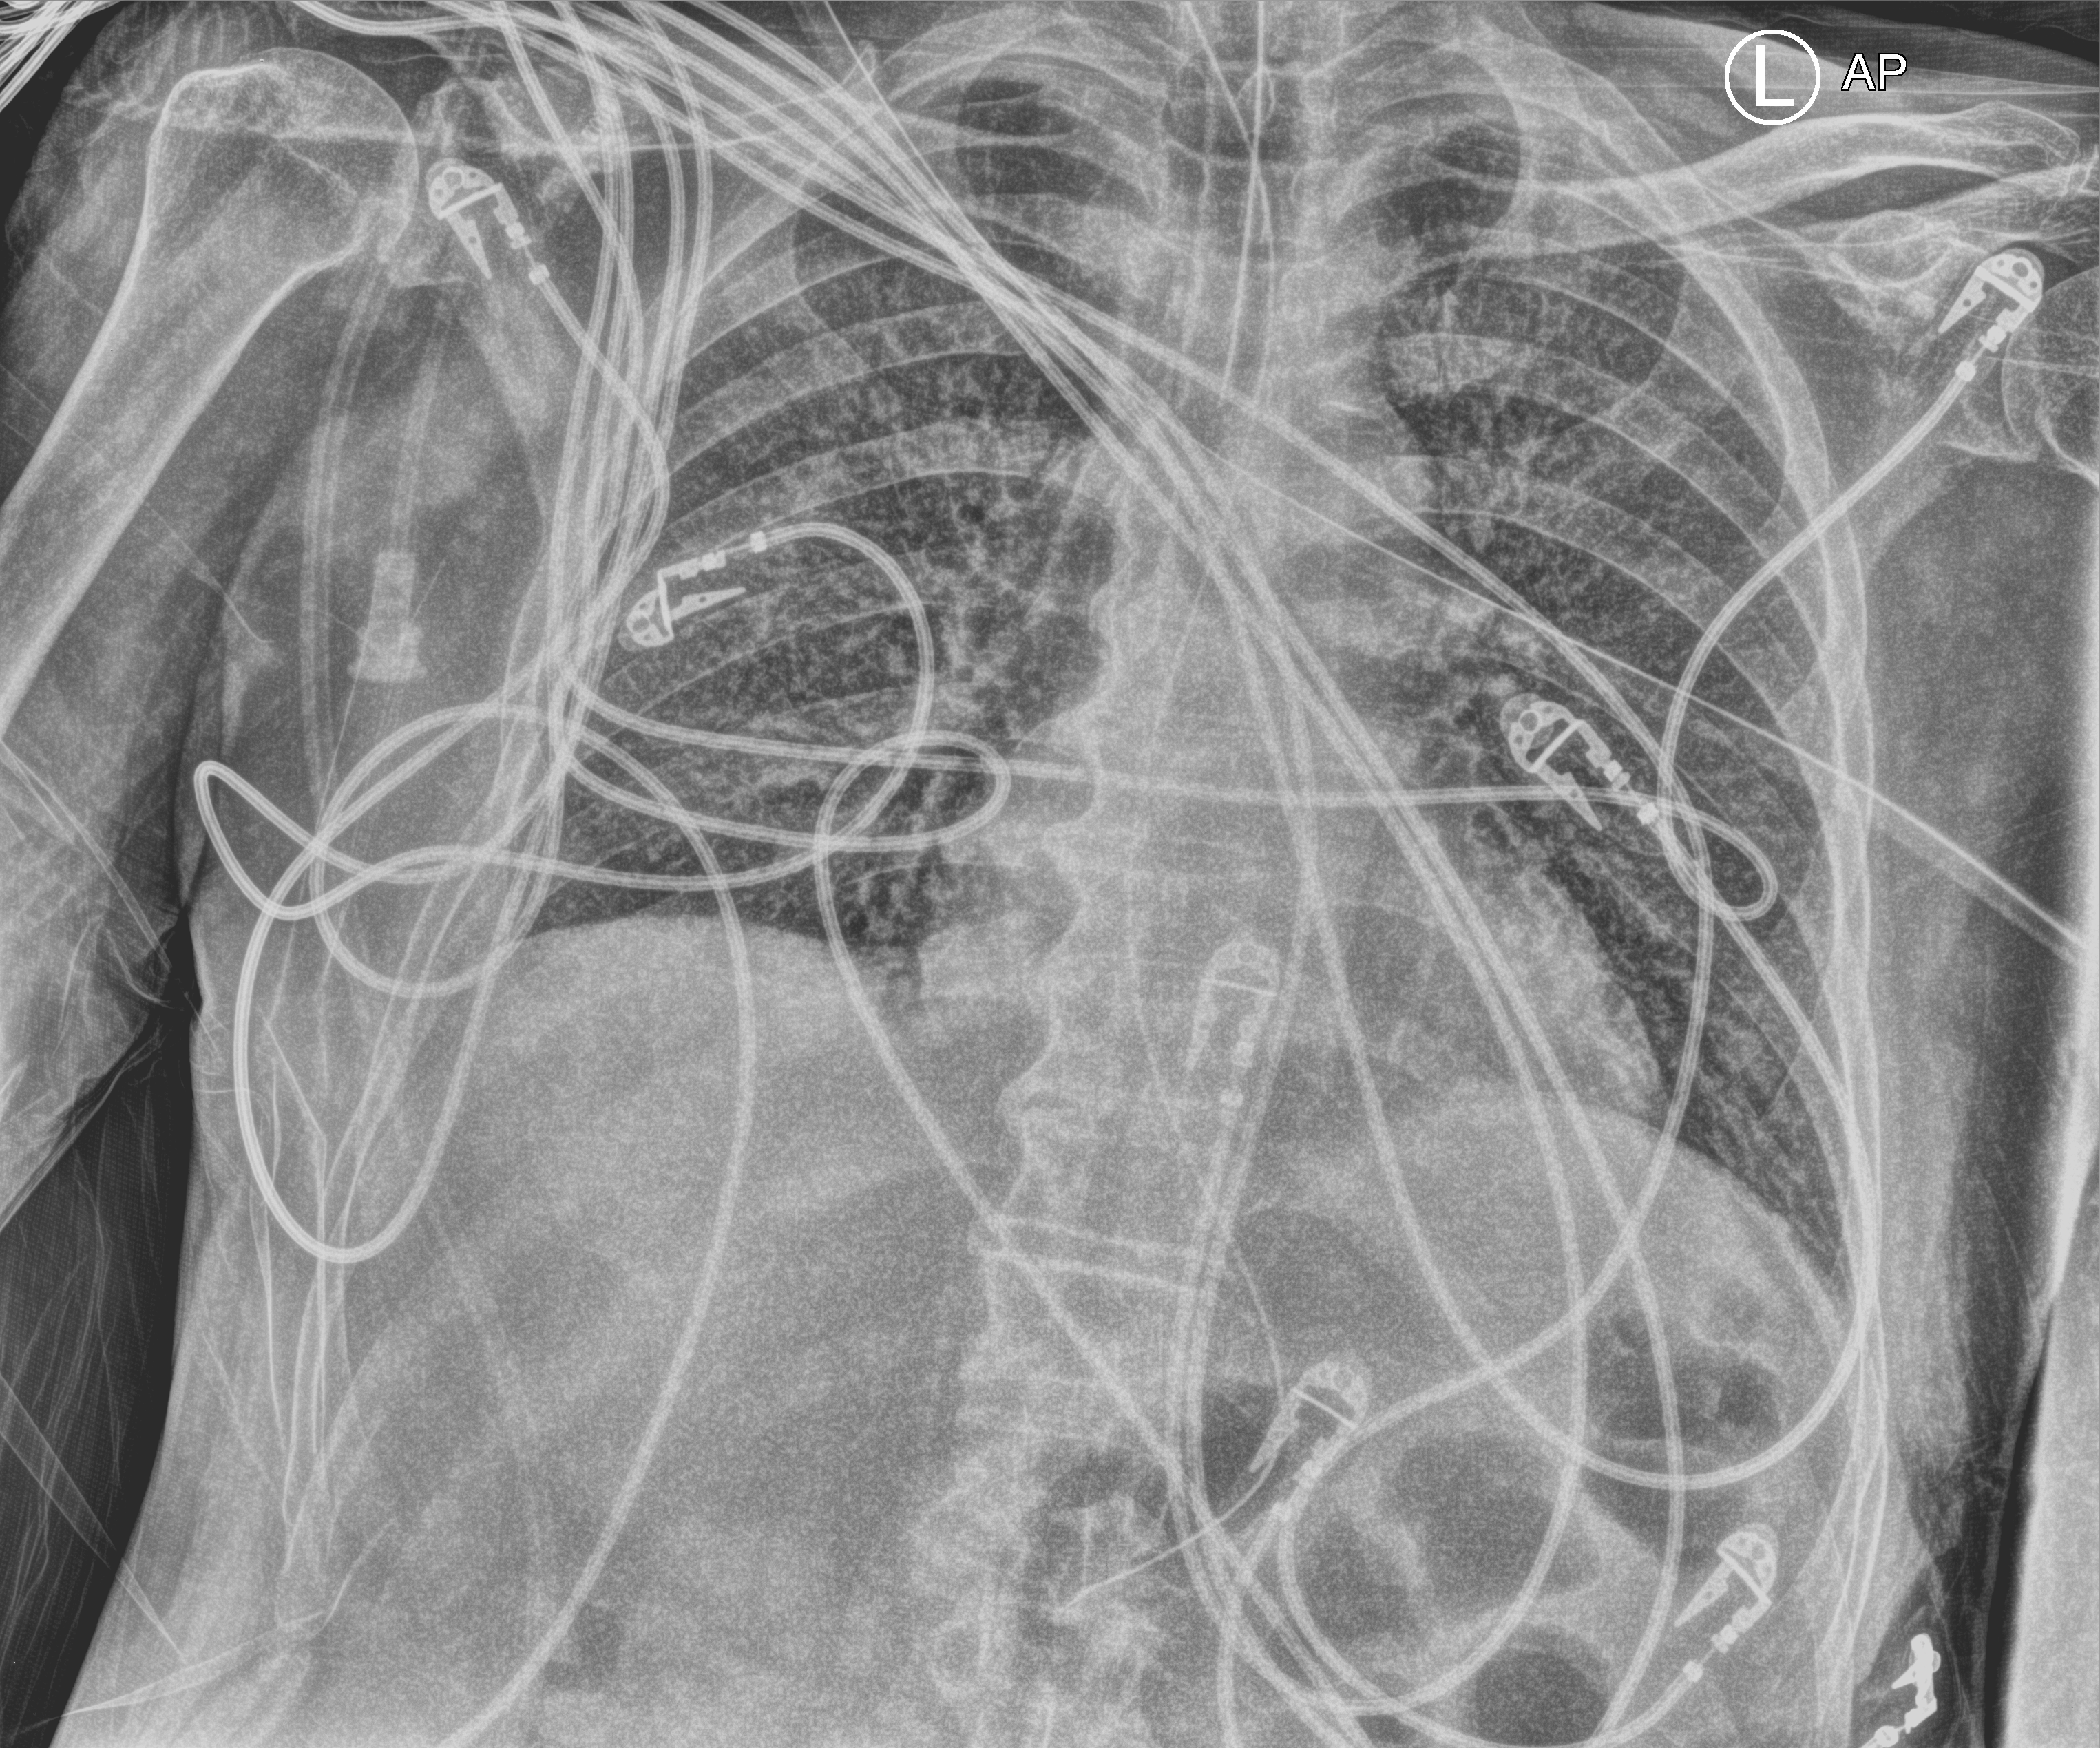
Chest X-ray (portable); anteroposterior (AP) projection. Patient hospitalised with COVID-19; male, aged 75–90 years.
From the hospital-stay record, not from the radiograph (when in the stay this image was taken is not recorded): admitted to intensive care during this hospital stay: yes.